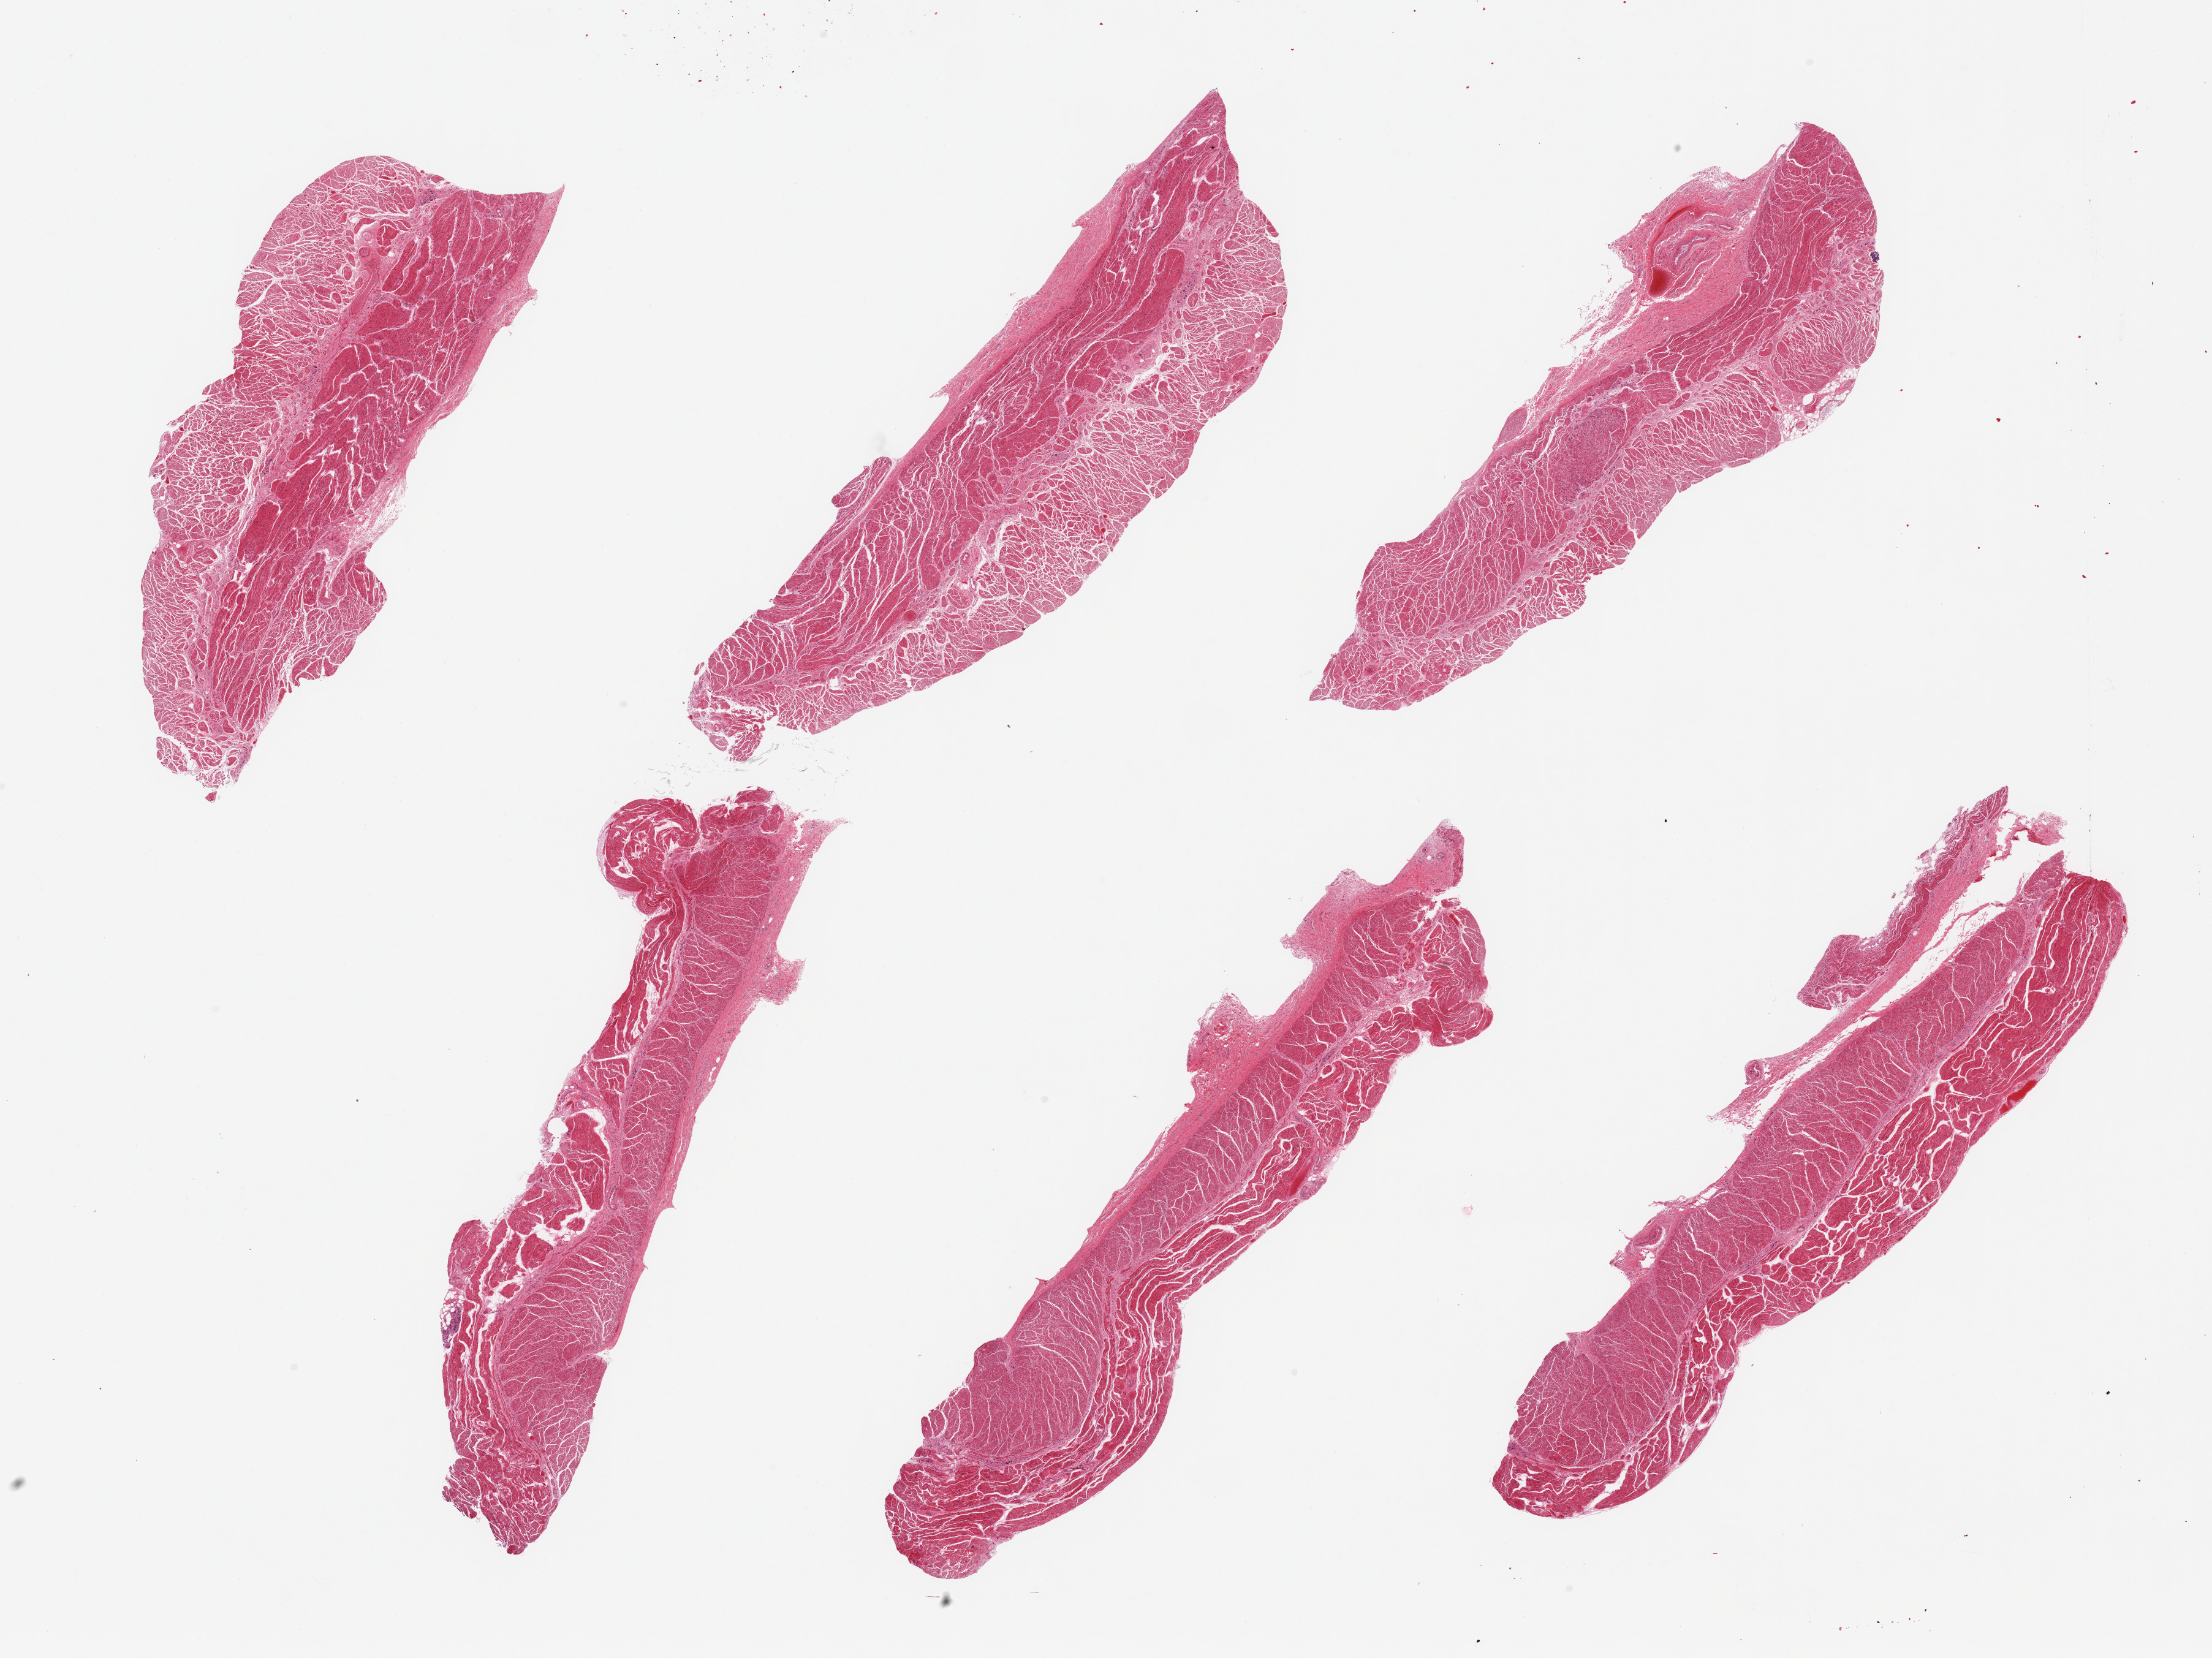
H&E whole-slide image — low-resolution overview of the scanned area, about 28.5 x 21.4 mm, PAXgene-fixed, paraffin-embedded tissue, sampled site (target tissue): esophageal muscle, donor tissue sample. Male donor.
Pathologist's review note for this sample: 6 pieces, confirmed target muscularis.